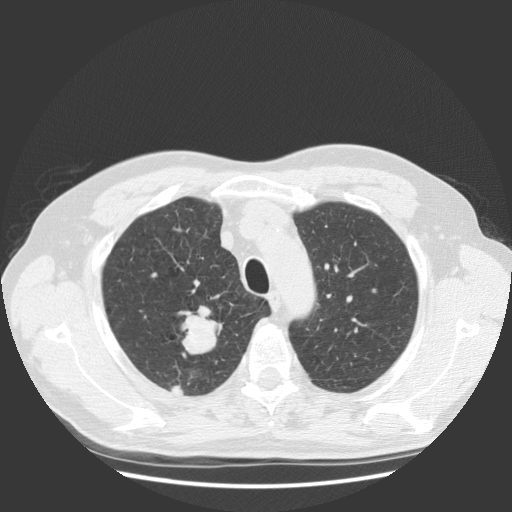
Low-dose screening chest CT, one axial slice; position 100 of 131 along the scan axis; lung window (W 1500 / L -600 HU); 512 × 512 image matrix, field of view 369 × 369 mm.
Annotated regions visible in this slice (expert manual segmentation):
- lesion 1 (tumor, upper lobe of right lung): bounding box <178,306,222,355> (left, top, right, bottom; pixels)
- lesion 2 (tumor, upper lobe of right lung): <171,385,183,394>